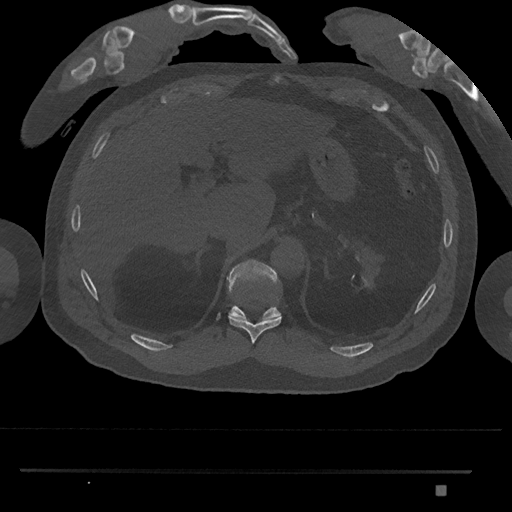
CT including the spine, one axial slice. Position 981 of 1134 along the scan axis. Reconstruction kernel Br40s/3. 120 kVp. Bone window (W 1800 / L 400 HU). 0.5 mm slice thickness. 512 × 512 image matrix, field of view 429 × 429 mm. Male patient, age 65 years. From the clinical record (not read from this slice): primary cancer: prostate.
Structures marked on this image (semi-automatically segmented with operator editing):
- T10 vertebra: bounding box <228,296,282,344> (left, top, right, bottom; pixels)
- T11 vertebra: <226,259,281,321>